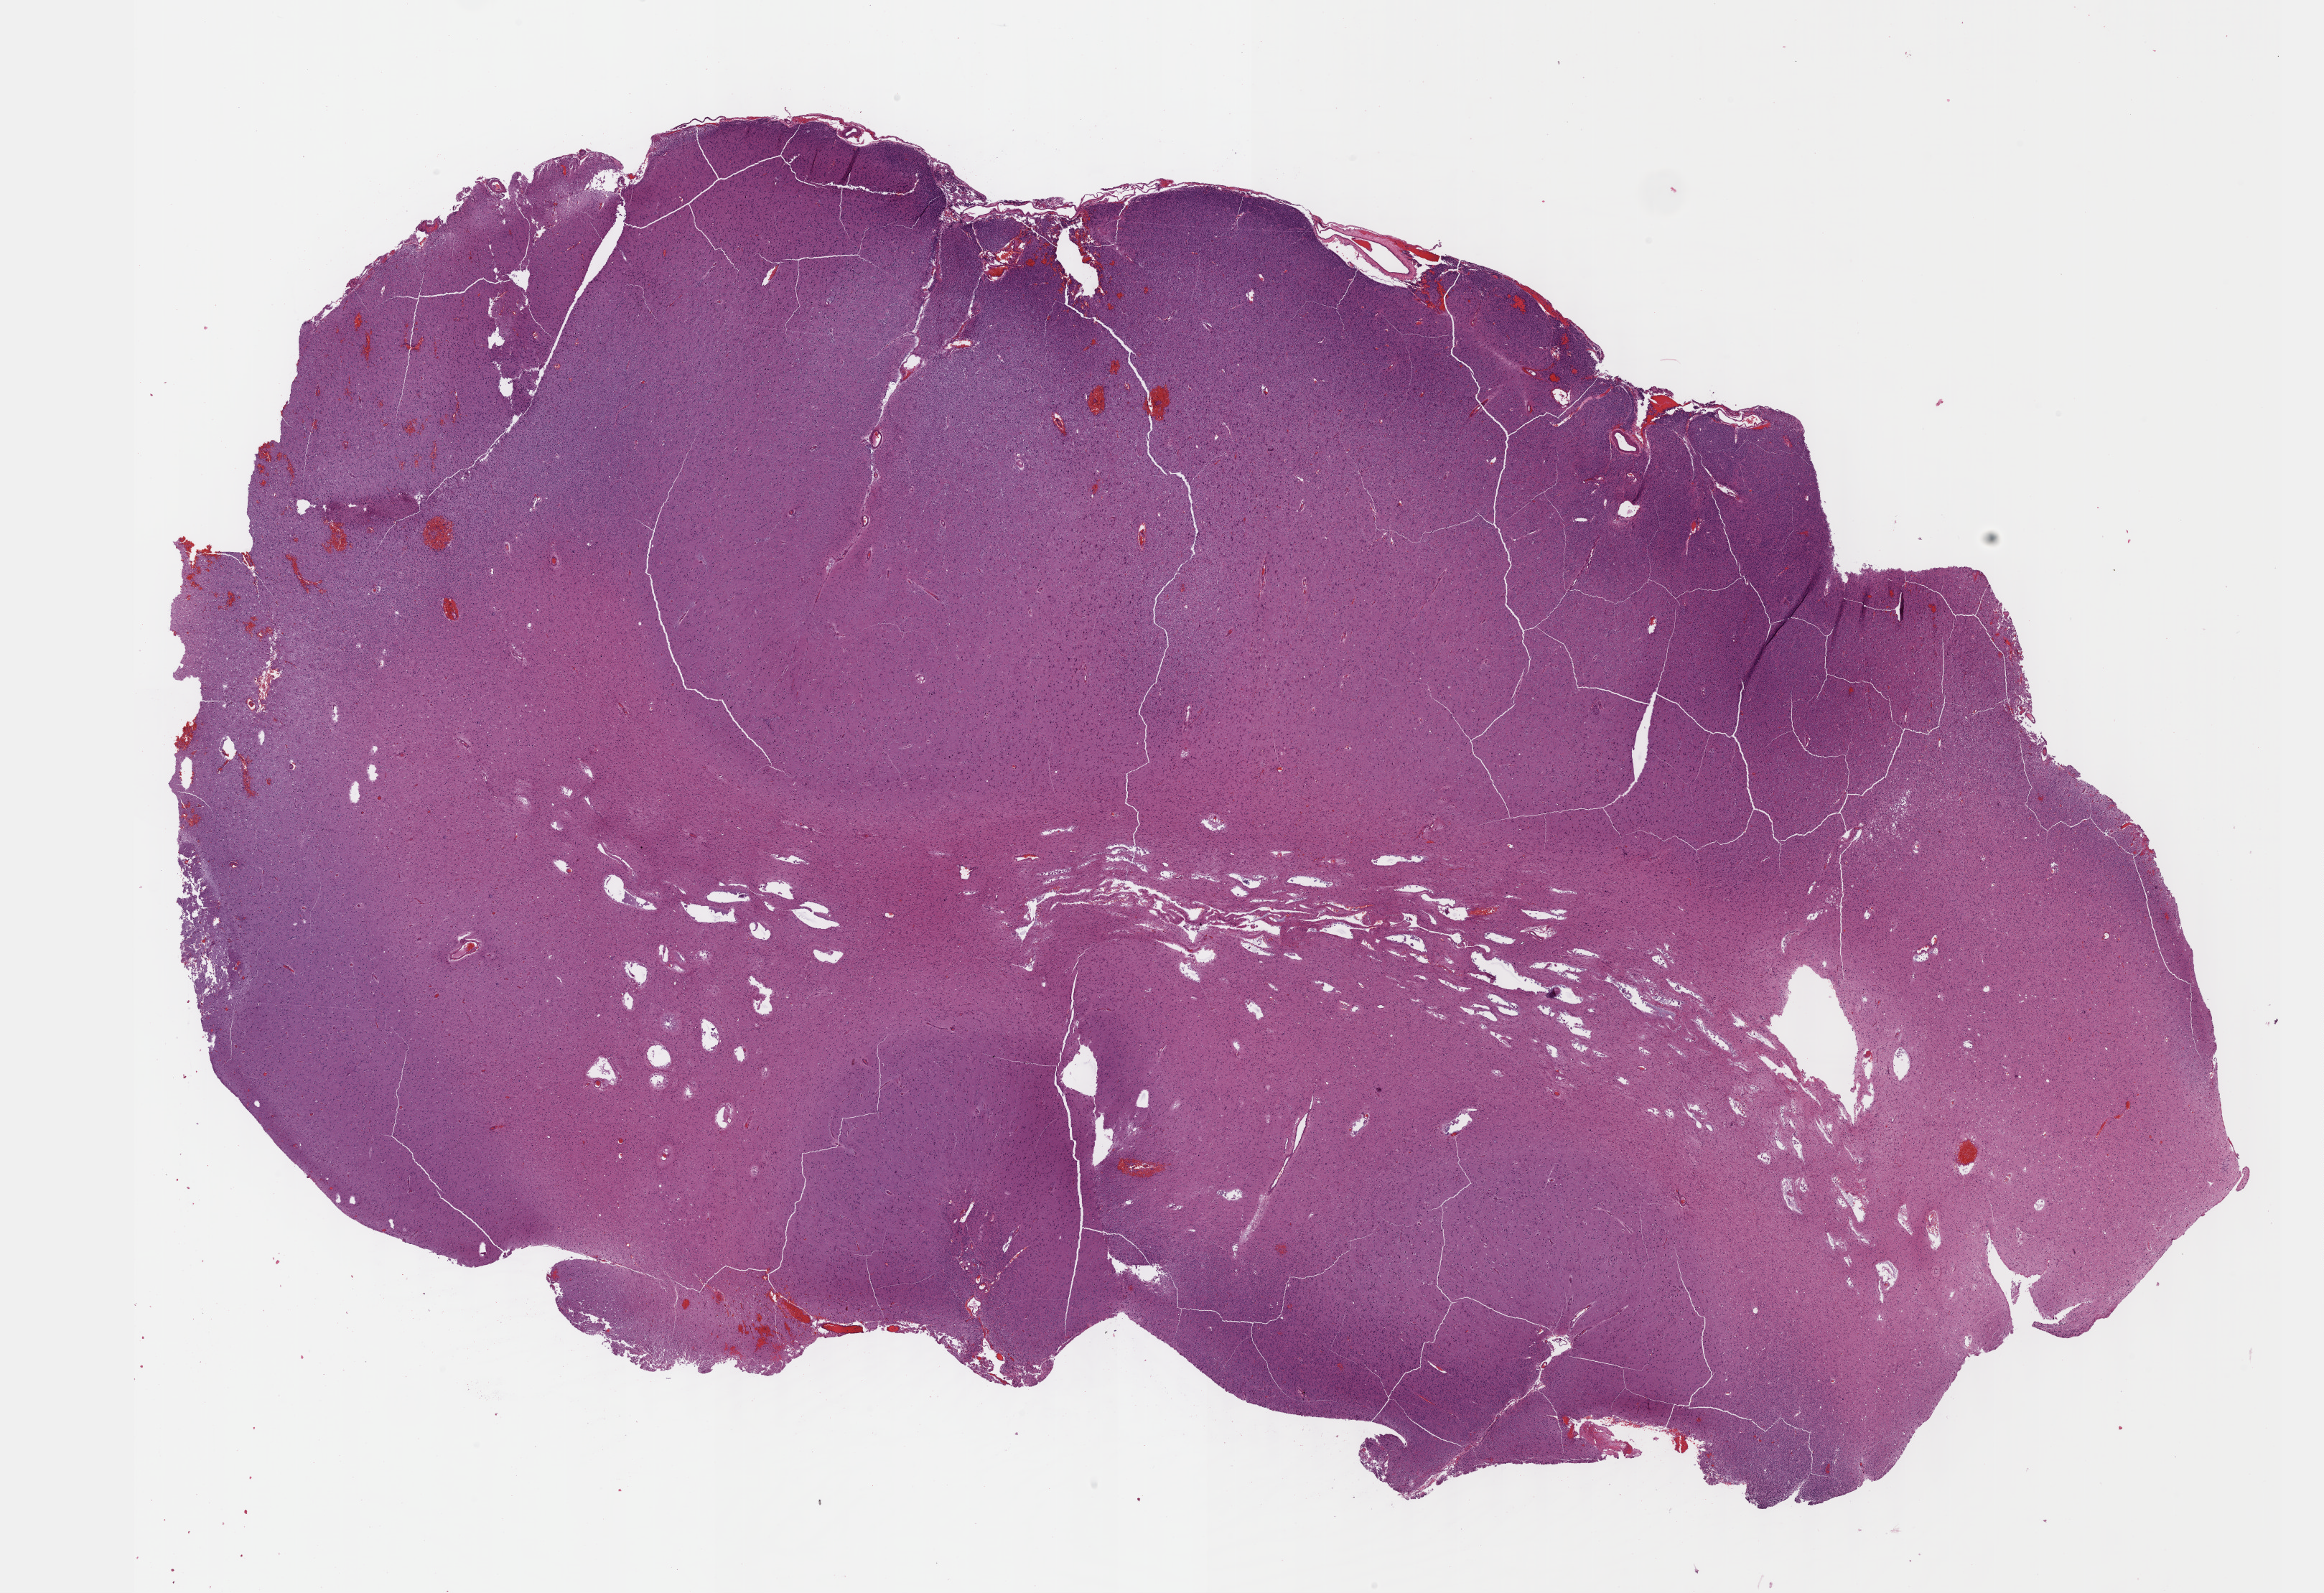
Hematoxylin and eosin (H&E) stained whole-slide image — whole scanned area (about 26.2 x 17.9 mm, from a 40x scan) shown as a low-resolution overview; formalin-fixed paraffin-embedded (FFPE) diagnostic section; primary tumour sample from the brain. Patient: male, age at initial diagnosis 60 years. Histologic grade: G3 (poorly differentiated).
Histologic diagnosis: Oligodendroglioma, anaplastic (cerebrum). Laterality: right.